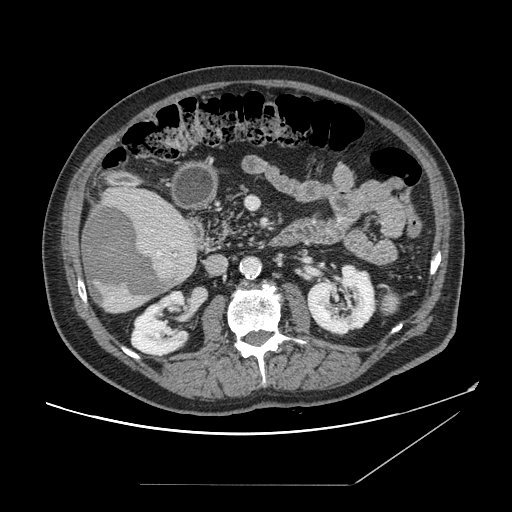
Contrast-enhanced abdominal CT, one axial slice. Position 63 of 166 along the scan axis. Soft-tissue window (W 400 / L 40 HU). 512 × 512 image matrix. Male patient, age 80 years. From the clinical record (not read from this slice): diagnosis: colorectal cancer liver metastases, imaged before liver resection; multiple liver metastases: no; largest metastasis: 2.2 cm; disease in both lobes: no.
Structures marked on this image (expert manual segmentation):
- liver: bounding box (x1, y1, x2, y2) in pixels: (81, 187, 199, 314)
- planned liver remnant (the part of the liver to remain after resection): (128, 188, 172, 210)
- liver metastasis: (84, 205, 169, 307)